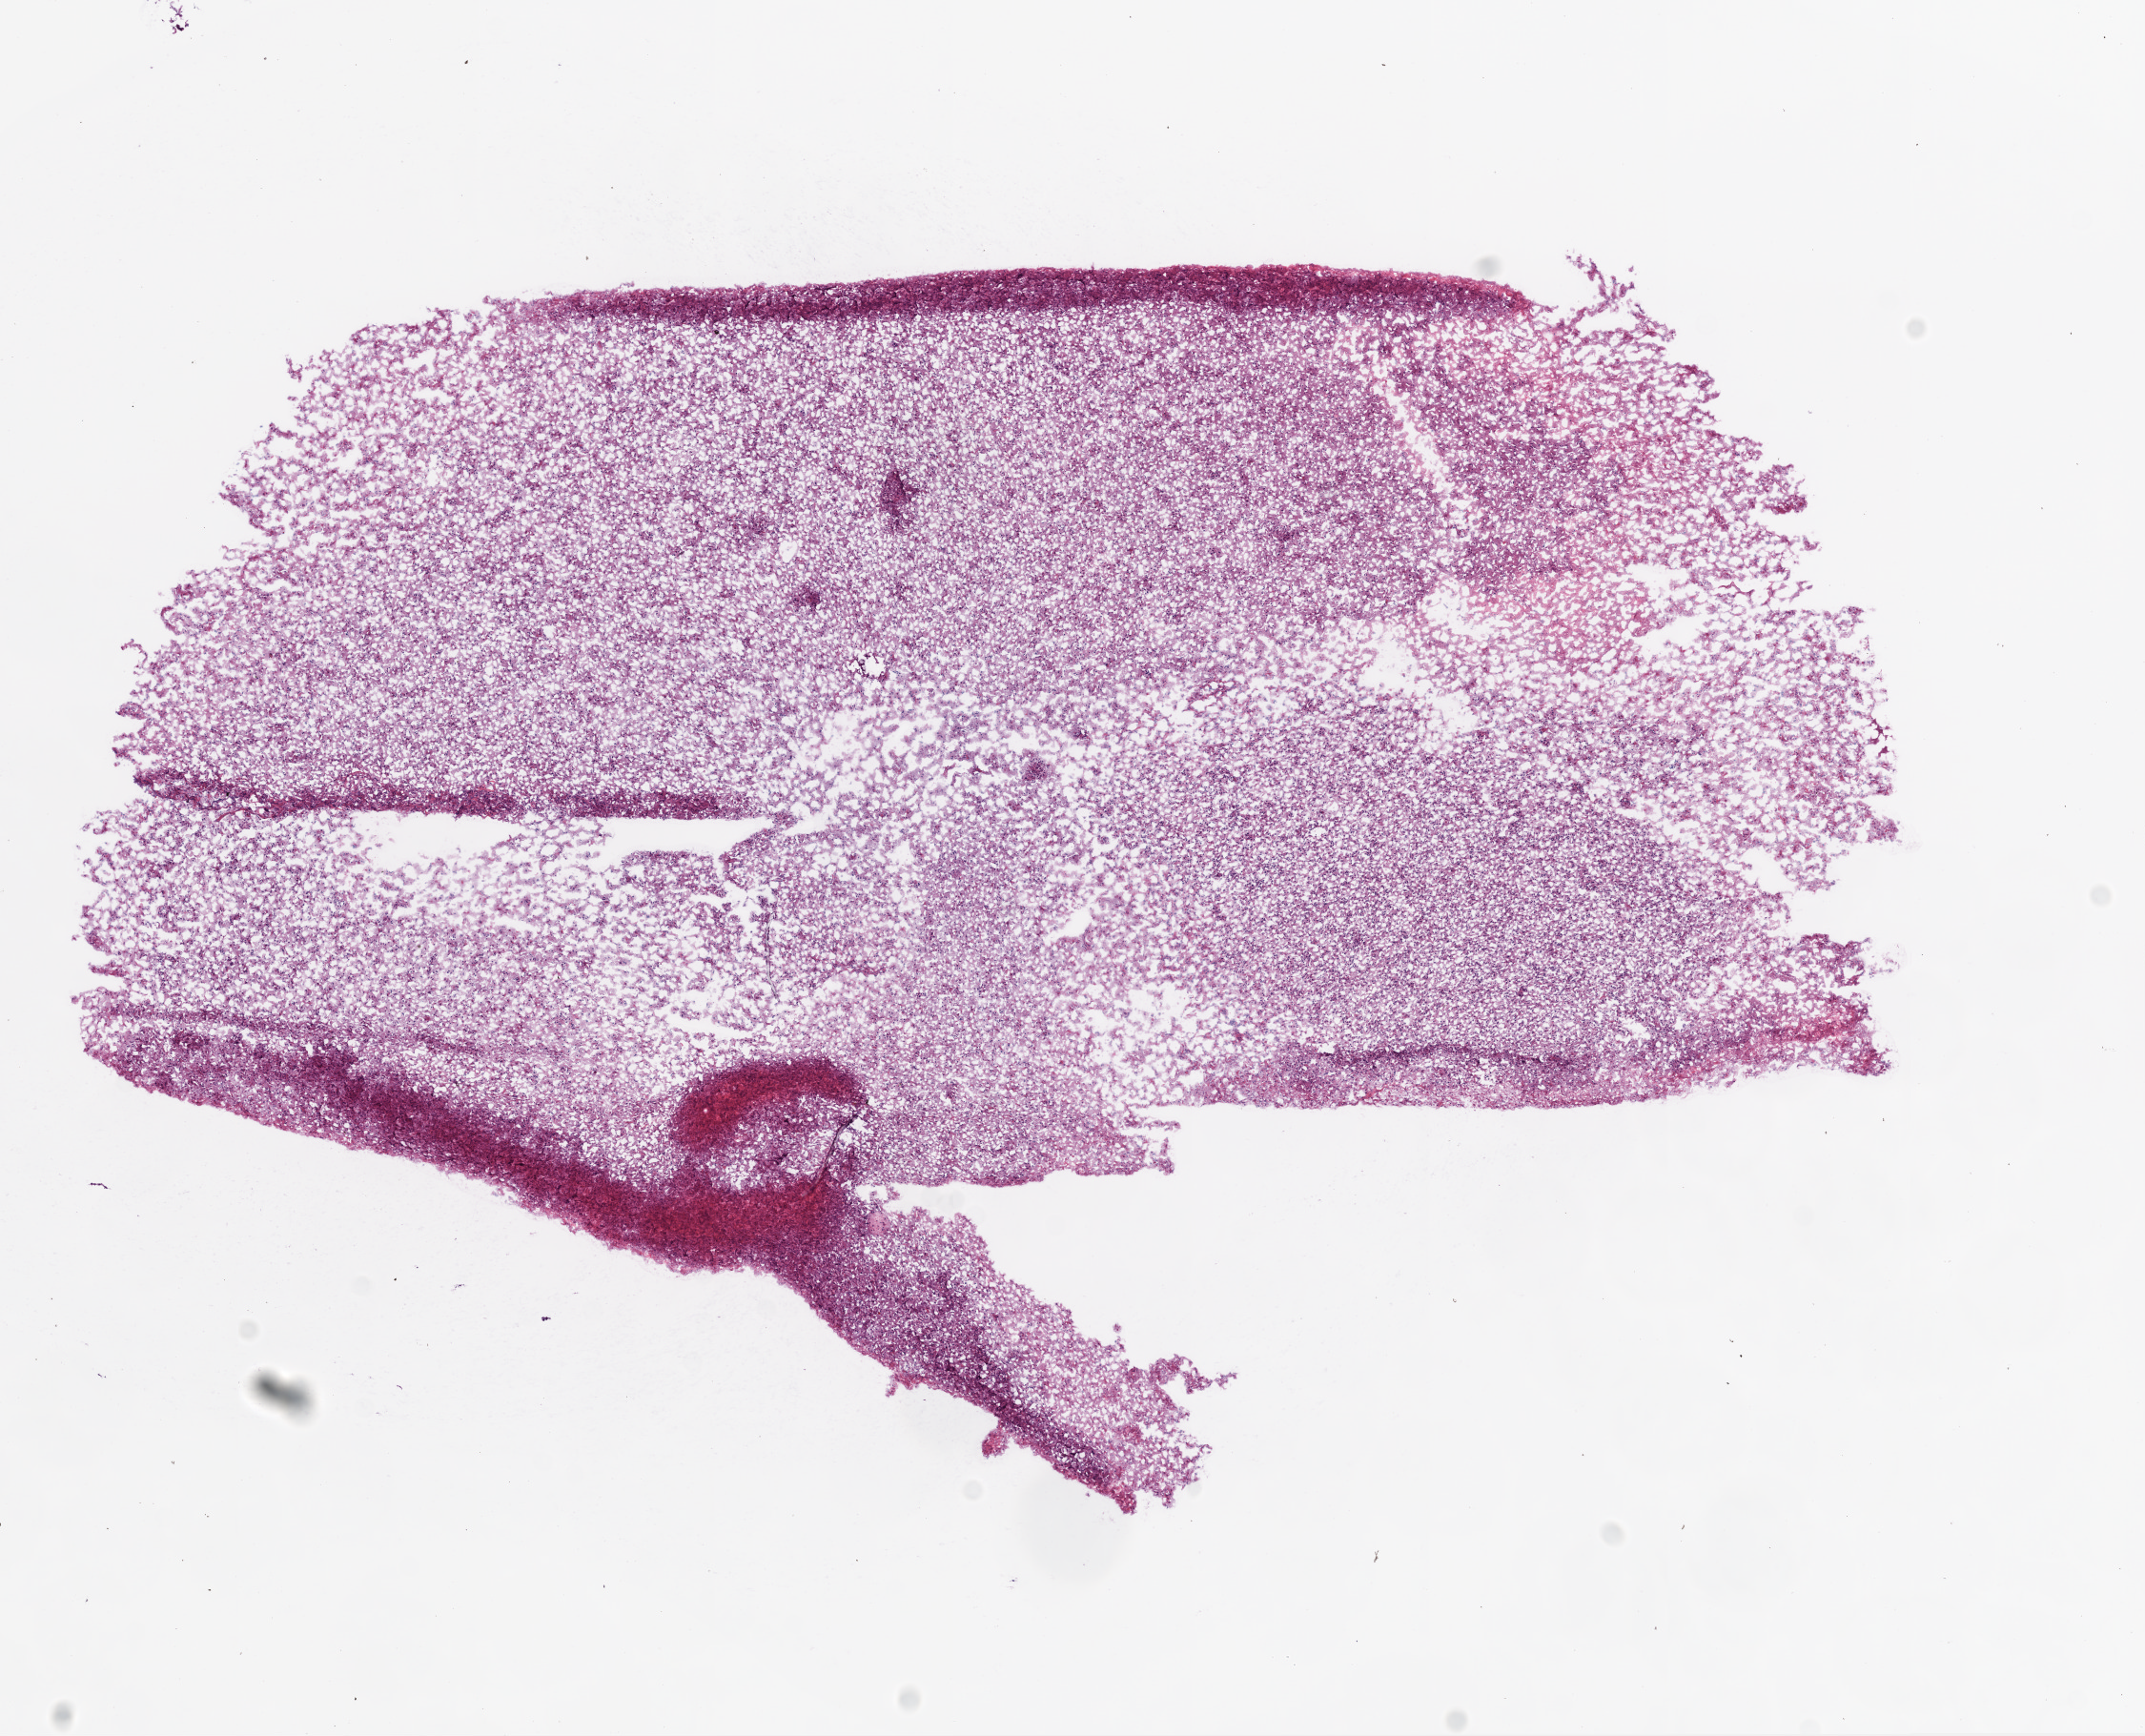
H&E-stained whole-slide image, whole scanned area (about 9.0 x 7.3 mm) shown as a low-resolution overview. Frozen section. Sample: primary tumour, brain. Male, age 44 years at initial diagnosis. Composition of this section per pathologist review: tumour cells 100%, tumour nuclei 80%, normal cells 0%, stromal cells 0%, necrosis 0%.
Diagnosis: Glioblastoma.